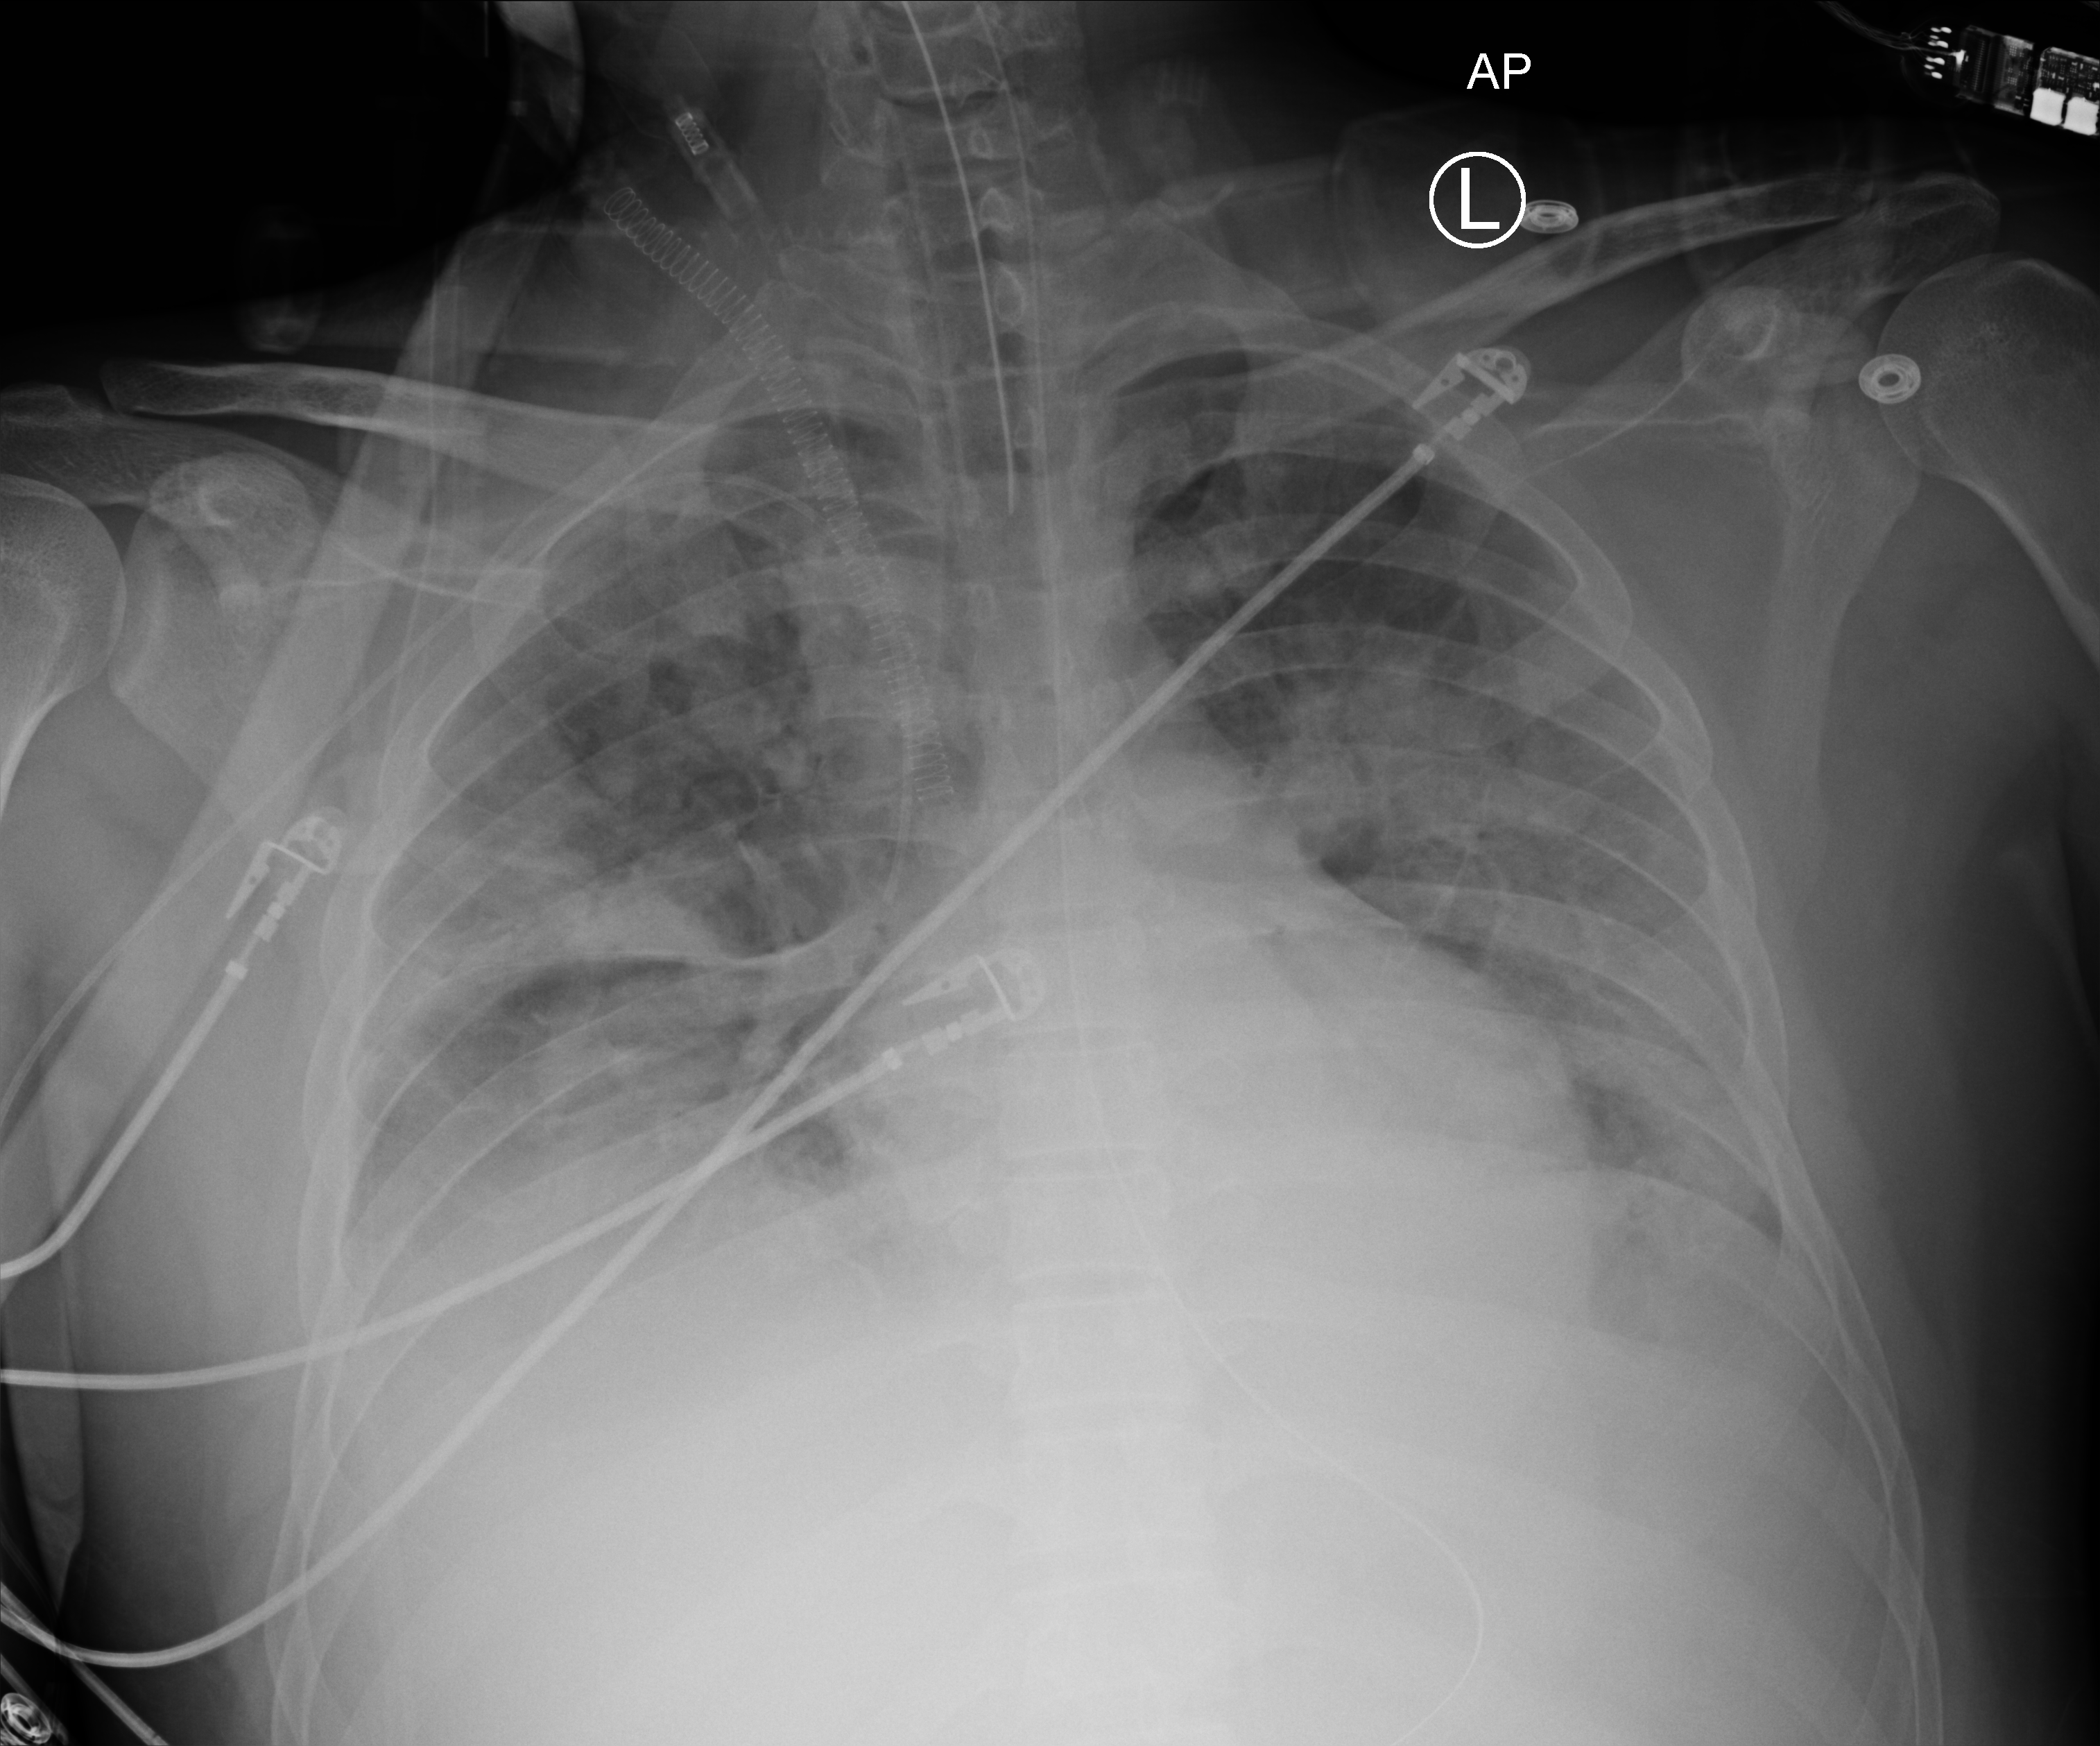
Bedside chest radiograph (computed radiography), anteroposterior (AP) projection. Adult patient hospitalised with COVID-19, age 18–59 years.
Hospital-stay facts (about this admission, not read from this image; timing relative to this image not recorded): admitted to intensive care during this hospital stay: yes; other chronic lung disease (admission record): no; length of hospital stay: 60 days.